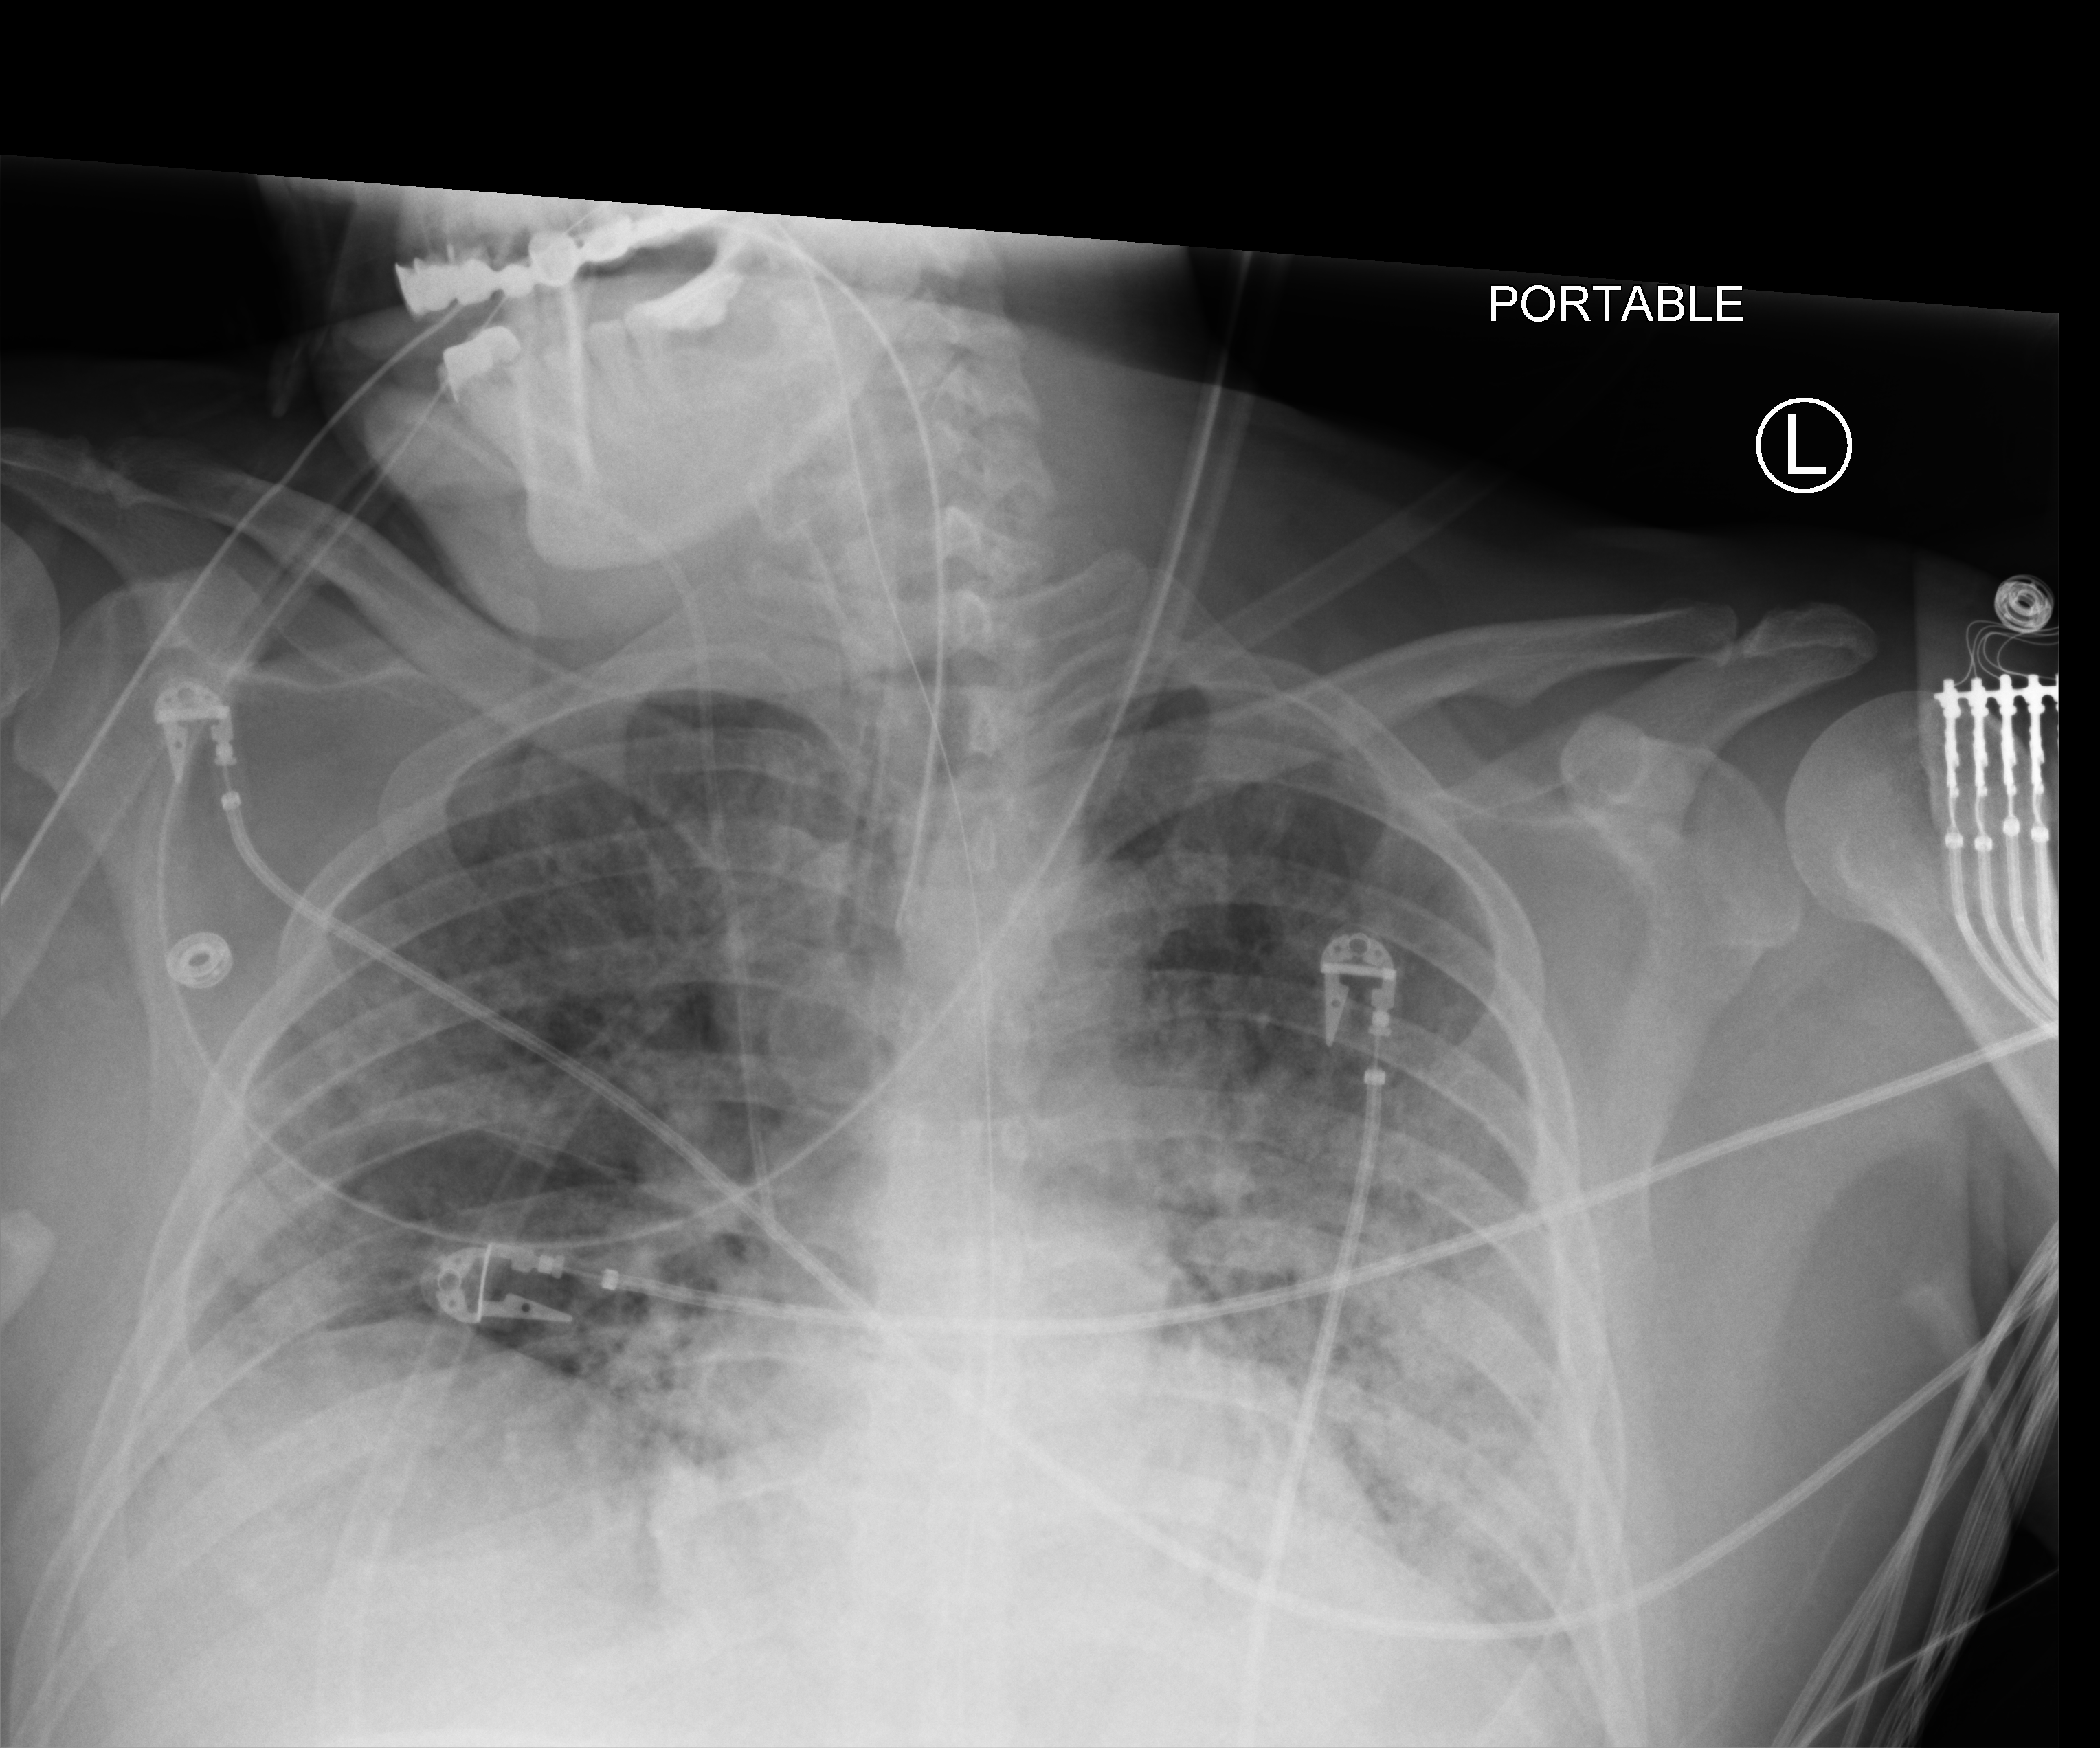
Chest X-ray (portable); anteroposterior (AP) projection. Patient hospitalised with COVID-19; male, aged 18–59 years.
From the hospital-stay record, not from the radiograph (when in the stay this image was taken is not recorded):
- COPD (admission record): no
- mechanically ventilated during this hospital stay: yes
- chronic kidney disease (admission record): no